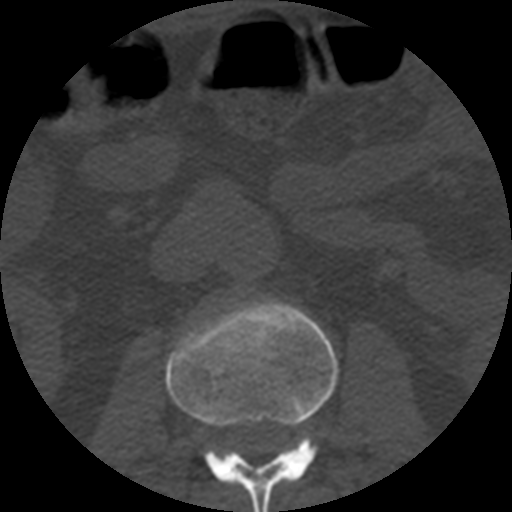
CT including the spine, one axial slice; position 146 of 508 along the scan axis; 120 kVp; bone window (W 1800 / L 400 HU); 1.25 mm slice thickness; 512 × 512 image matrix. Patient age 57 years. Case-level facts recorded for this patient, not image findings: primary cancer: prostate.
Annotated regions visible in this slice (semi-automatically segmented with operator editing):
- L2 vertebra: bounding box <166,298,338,512> (left, top, right, bottom; pixels)